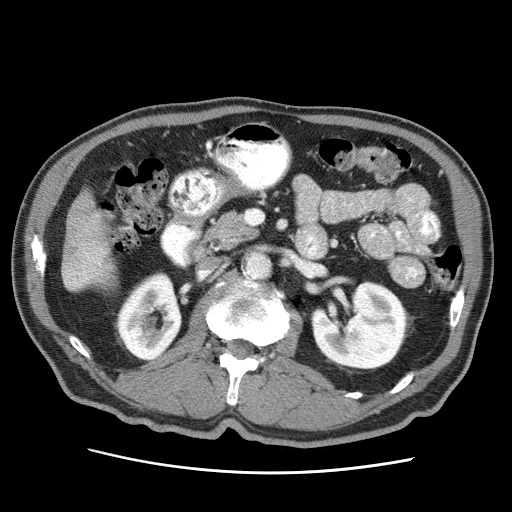
Contrast-enhanced abdominal CT (liver protocol), one axial slice; position 9 of 75 along the scan axis; soft-tissue window (W 400 / L 40 HU); 2.5 mm slice thickness; 512 × 512 image matrix, field of view 360 × 360 mm. From the clinical record (not read from this slice): diagnosis: hepatocellular carcinoma (patient treated with transarterial chemoembolisation; whether this scan precedes or follows treatment is not stated here); TNM stage (as recorded): Stage-IIIA; Child-Pugh class: A; tumour differentiation: well differentiated; tumour nodularity: multinodular.
Outlined on this slice (semi-automatically segmented with operator editing):
- liver parenchyma outside the tumour (the mass and vessels are separate outlines, so this box may not span the whole liver): bounding box (x1, y1, x2, y2) in pixels: (62, 190, 116, 290)
- liver vessels: (67, 252, 100, 285)